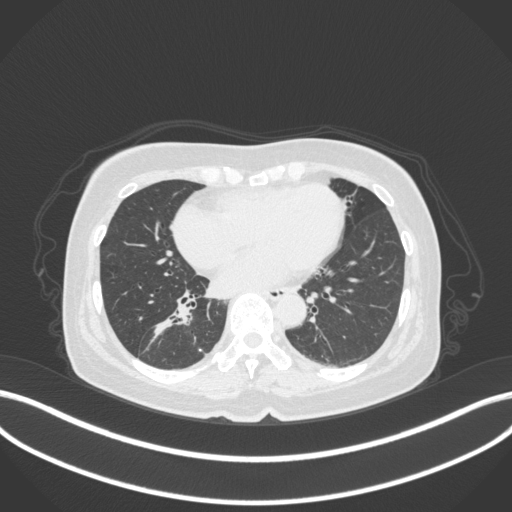
Chest CT, one axial slice; reconstruction kernel B31f; lung window (W 1500 / L -600 HU); 512 × 512 image matrix, field of view 400 × 400 mm. Female patient, age 67 years. From the clinical record (not read from this slice): clinical TNM (as recorded): T1c N1 M0.
Structures marked on this image (bounding box drawn by a radiologist):
- lung tumour (recorded histology: adenocarcinoma): bounding box <146,306,195,342> (left, top, right, bottom; pixels)